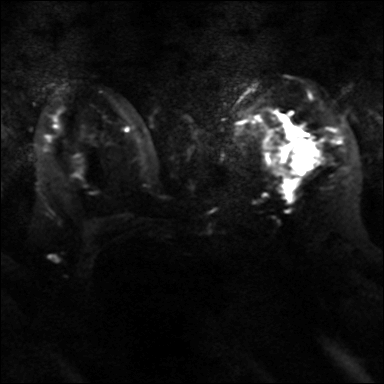
Breast MRI, one axial slice; slice 24 of 40 in the series (ordered by position); diffusion-weighted series; image 2 of 4 stored at this slice position (different b-values; order by instance number); 3 T; 4 mm slice thickness; 384 × 384 image matrix, field of view 320 × 320 mm. Female patient.
Outlined on this slice (expert manual segmentation):
- tumour on diffusion-weighted imaging: bounding box (x1, y1, x2, y2) in pixels: (290, 139, 320, 175)